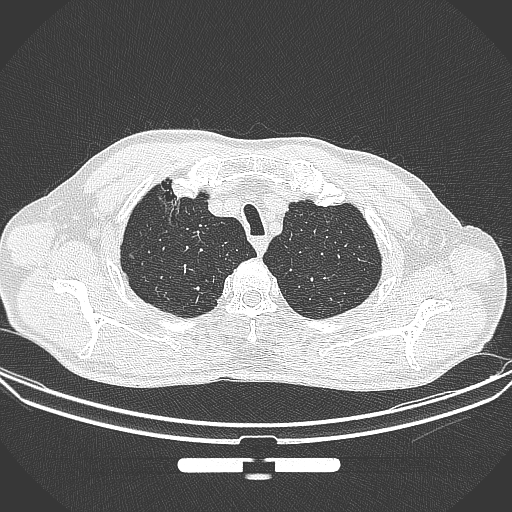
Chest CT, one axial slice. Position 297 of 355 along the scan axis. 120 kVp. Lung window (W 1500 / L -600 HU). 1 mm slice thickness. 512 × 512 image matrix. Male patient, age 67 years. Case-level facts recorded for this patient, not image findings: clinical TNM (as recorded): T1c N0 M0; histopathological grade: G2.
Outlined on this slice (rectangle marked by the reading radiologist):
- lung tumour (recorded histology: adenocarcinoma): bounding box [x1, y1, x2, y2] px = [156, 186, 182, 226]